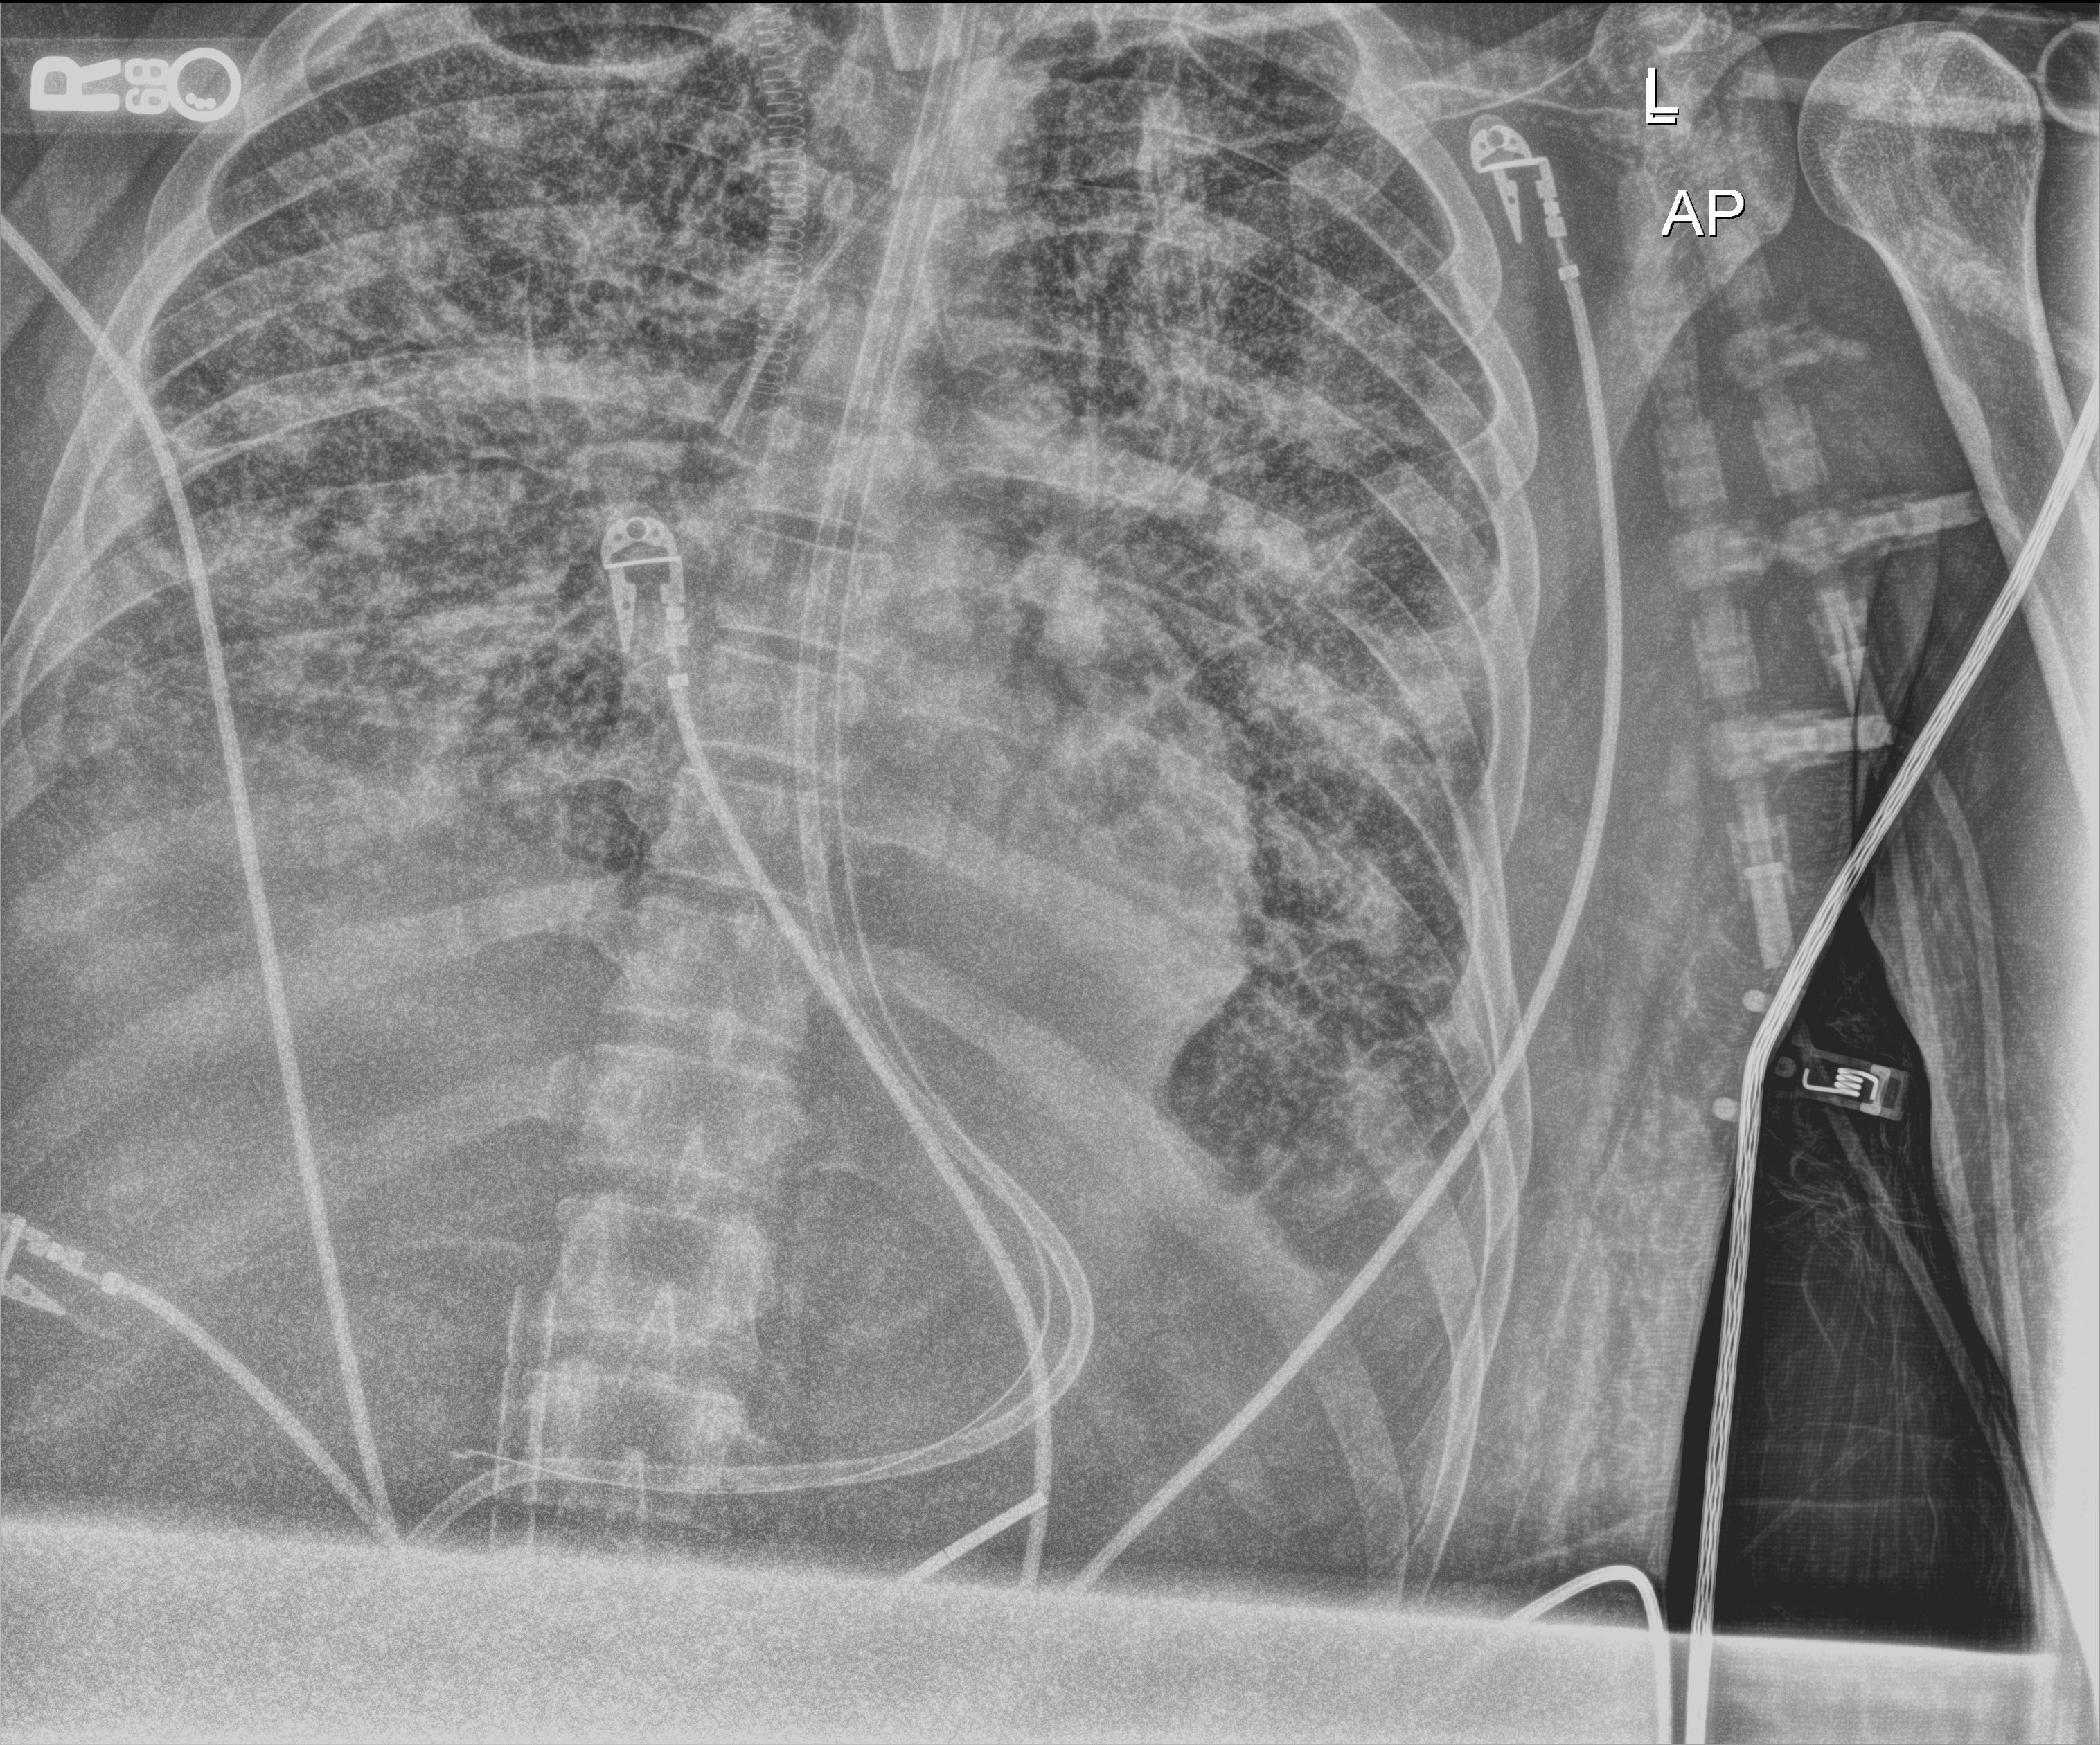
Chest radiograph (digital radiography), anteroposterior (AP) projection. Adult patient hospitalised with COVID-19, age 18–59 years.
Hospital-stay facts (about this admission, not read from this image; timing relative to this image not recorded): chronic kidney disease (admission record): no.